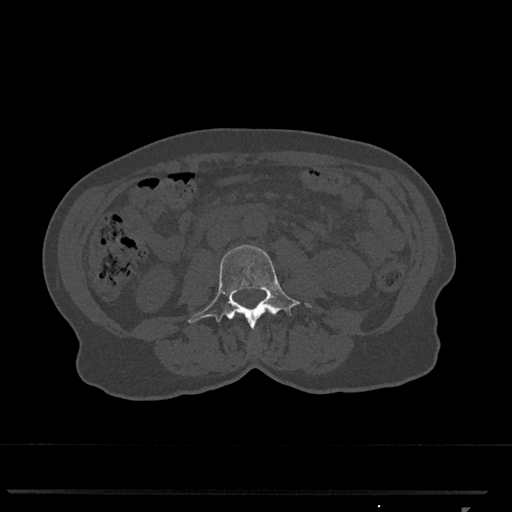
CT including the spine, one axial slice. Slice 278 of 793 in the series (ordered by position). Bone window (W 1800 / L 400 HU). 0.5 mm slice thickness. 512 × 512 image matrix. Female patient, age 62 years. From the clinical record (not read from this slice): primary cancer: renal.
Structures marked on this image (semi-automatic segmentation, software-assisted and operator-edited):
- L3 vertebra: bounding box <188,245,312,330> (left, top, right, bottom; pixels)